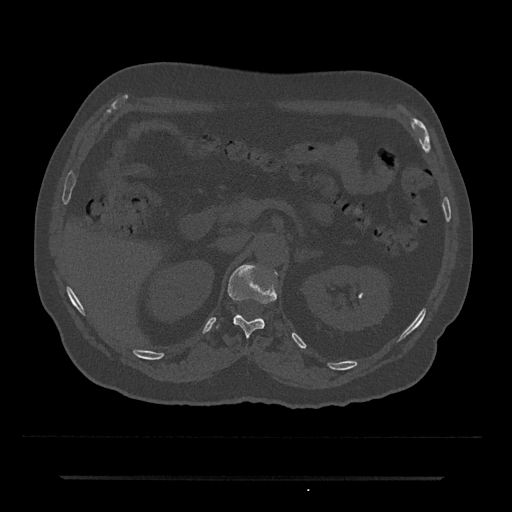
CT including the spine, one axial slice. Slice 119 of 797 in the series (ordered by position). Bone window (W 1800 / L 400 HU). 0.5 mm slice thickness. 512 × 512 image matrix, field of view 437 × 437 mm. Male patient, age 69 years. Case-level facts recorded for this patient, not image findings: primary cancer: prostate.
Outlined on this slice (semi-automatically segmented with operator editing):
- T12 vertebra: bounding box [x1, y1, x2, y2] px = [216, 264, 277, 338]